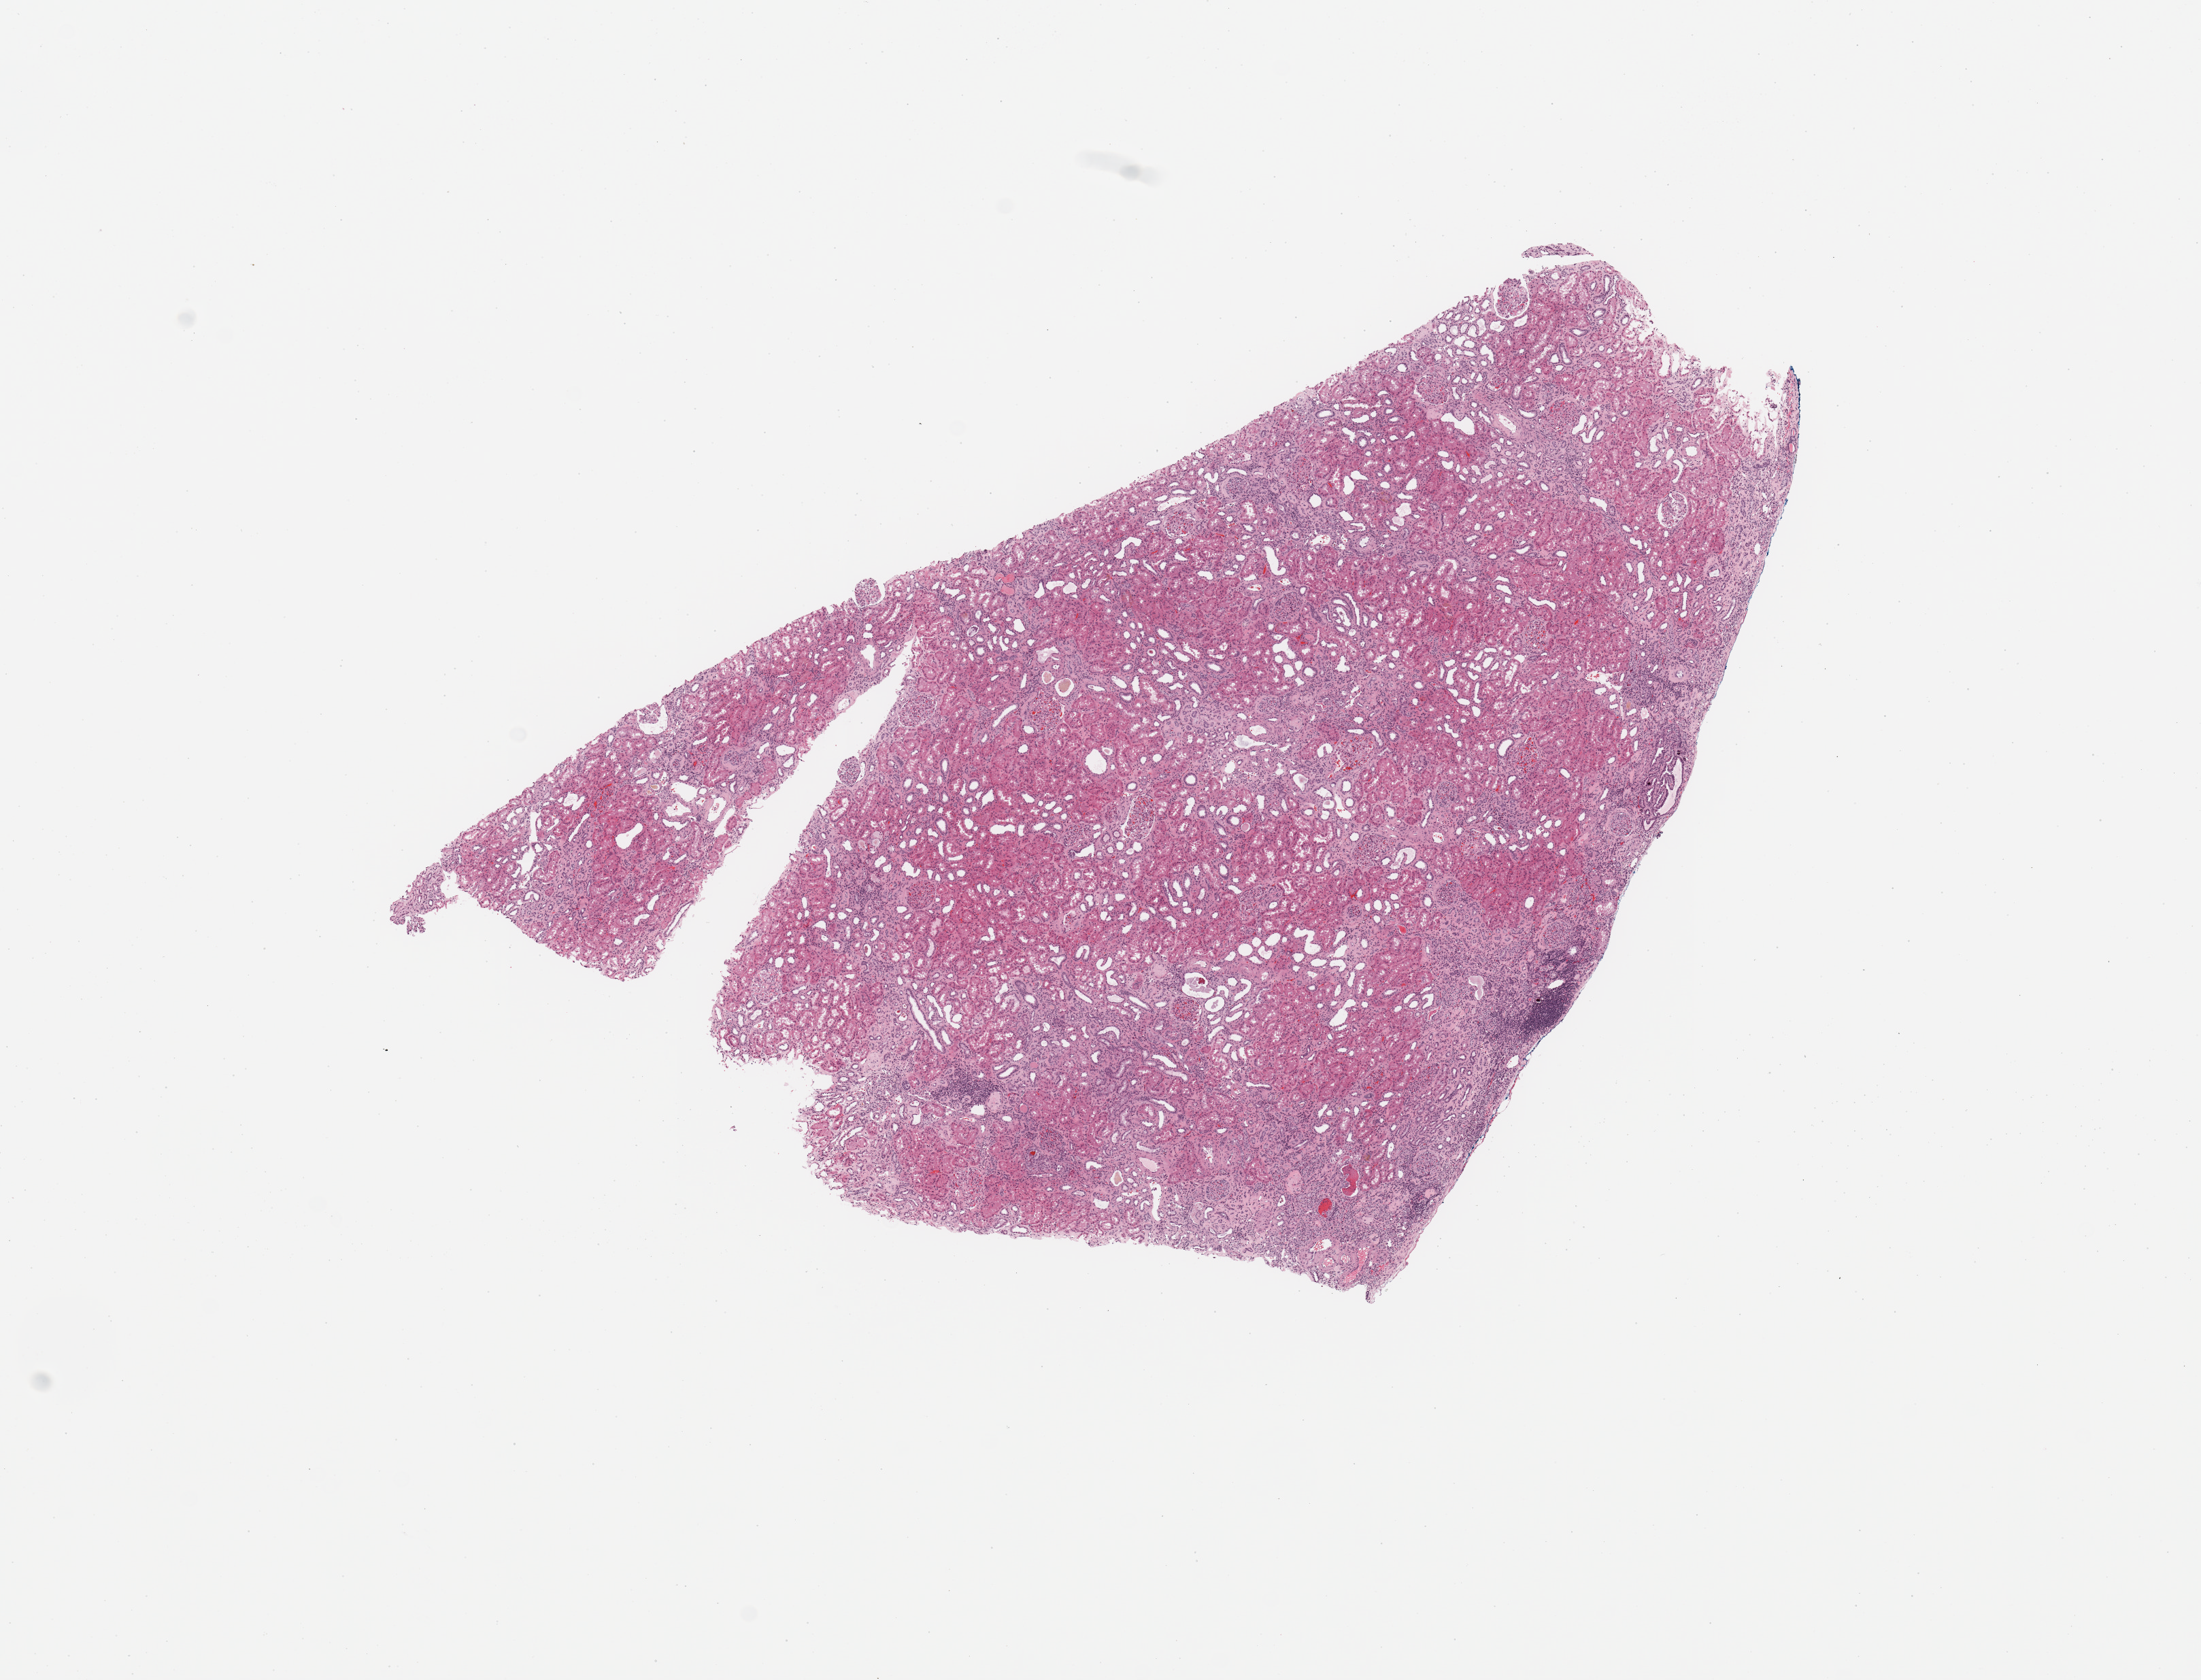
Digitized H&E tissue section (whole slide), shown as a low-resolution overview of the whole scanned area (about 12.8 x 9.8 mm, from a 20x scan). Normal (non-tumour) tissue sample, sampled site: kidney. Male, 67 y/o.
This section: normal (non-tumour) tissue from the same patient. Patient diagnosis: Renal cell carcinoma, NOS.